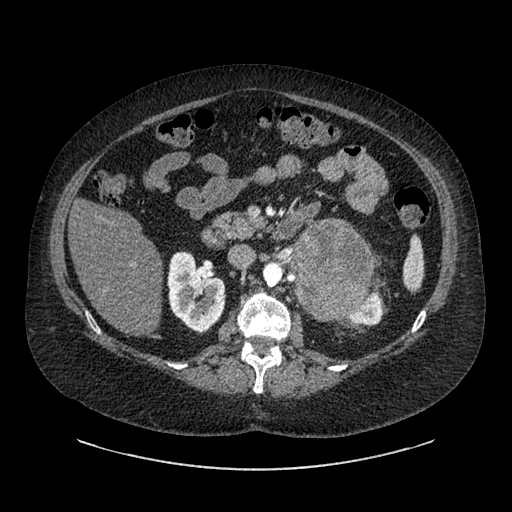
Contrast-enhanced abdominal CT, one axial slice; slice 528 of 769 in the series (ordered by position); 120 kVp; intravenous contrast given; soft-tissue window (W 400 / L 40 HU); 0.62 mm slice thickness; 512 × 512 image matrix, field of view 460 × 460 mm. Patient: female, 61 years. Case-level facts recorded for this patient, not image findings: diagnosis: adrenocortical carcinoma; tumour side: left adrenal; tumour size at pathology: 13 cm; Ki-67 index: 79 %; stage (as recorded): 2.
Annotated regions visible in this slice (semi-automatic segmentation, software-assisted and operator-edited):
- mass: bounding box <291,221,373,316> (left, top, right, bottom; pixels)